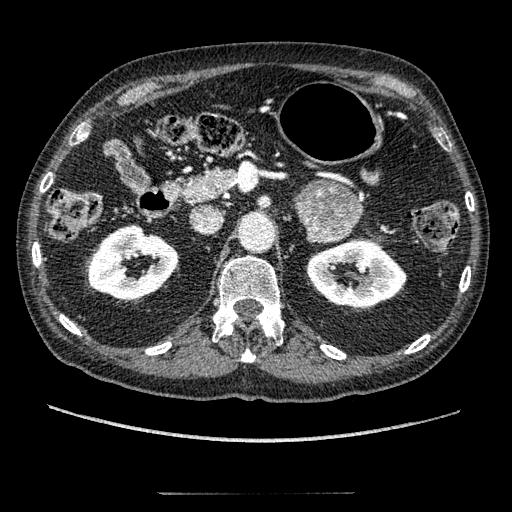
Contrast-enhanced abdominal CT, one axial slice; slice 118 of 274 in the series (ordered by position); reconstruction kernel STANDARD; 120 kVp; intravenous contrast given; soft-tissue window (W 400 / L 40 HU); 1.25 mm slice thickness; 512 × 512 image matrix. Patient: male, 69 years. Case-level facts recorded for this patient, not image findings: diagnosis: adrenocortical carcinoma; tumour side: left adrenal; tumour size at pathology: 6.1 cm; Ki-67 index: 10 %; stage (as recorded): 3.
Structures marked on this image (semi-automatically segmented with operator editing):
- mass: bounding box [x1, y1, x2, y2] px = [295, 181, 361, 239]